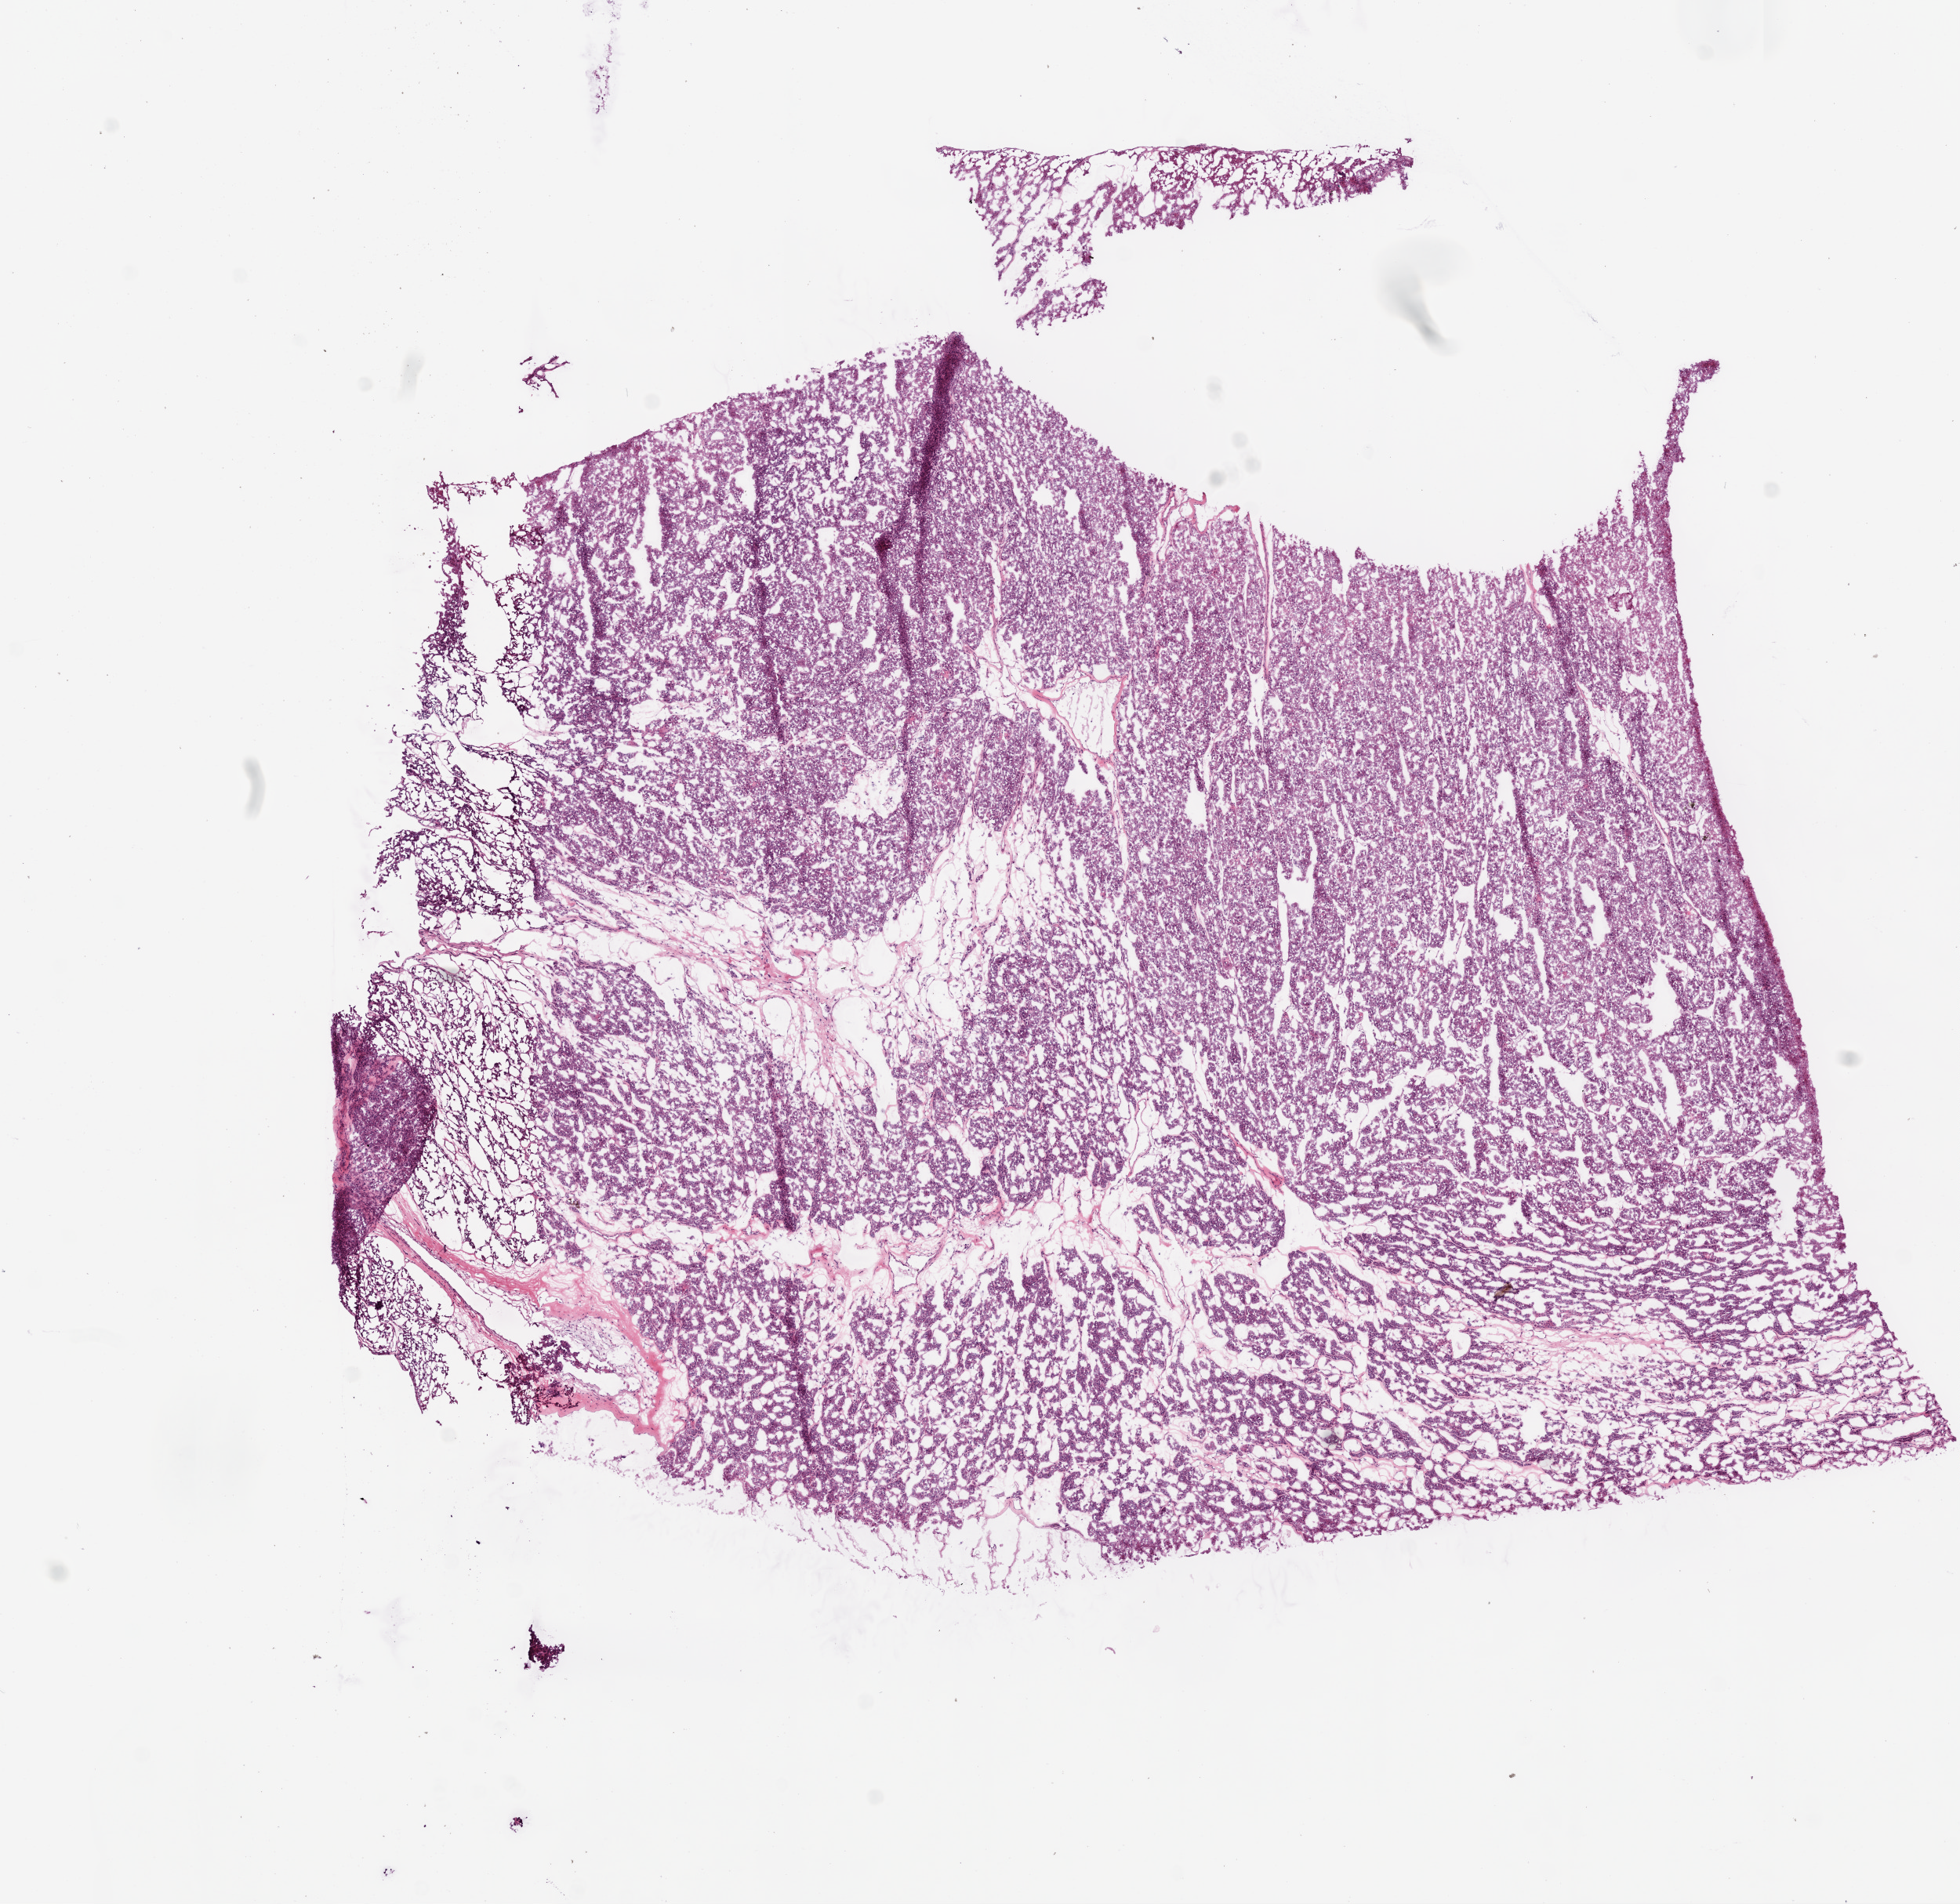
Digitized Hematoxylin and eosin (H&E) stained tissue section (whole slide), whole scanned area (about 10.0 x 9.7 mm) shown as a low-resolution overview; frozen section from the bottom of the tissue portion; kidney, primary tumour sample. Patient: male, age at initial diagnosis 65 years. Histologic grade: GX (grade cannot be assessed). Pathologist review of this section (percent, as recorded): tumour cells 90%, tumour nuclei 85%, normal cells 0%, stromal cells 10%, necrosis 0%.
AJCC pathologic stage: I. Lymph nodes positive (case pathology): 15 of 15 examined. Laterality: left. Histologic diagnosis: Clear cell adenocarcinoma, NOS.